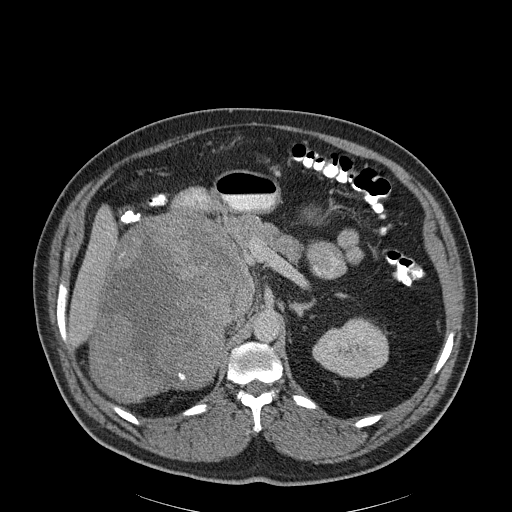
Contrast-enhanced abdominal CT, one axial slice. Slice 129 of 186 in the series (ordered by position). 120 kVp. Soft-tissue window (W 400 / L 40 HU). 3 mm slice thickness. 512 × 512 image matrix, field of view 464 × 464 mm. Male patient, age 56 years. From the clinical record (not read from this slice): diagnosis: adrenocortical carcinoma; tumour side: right adrenal; tumour size at pathology: 18 cm; Ki-67 index: 2 %; stage (as recorded): 3.
Outlined on this slice (semi-automatic segmentation, software-assisted and operator-edited):
- mass: bounding box (x1, y1, x2, y2) in pixels: (92, 218, 249, 400)